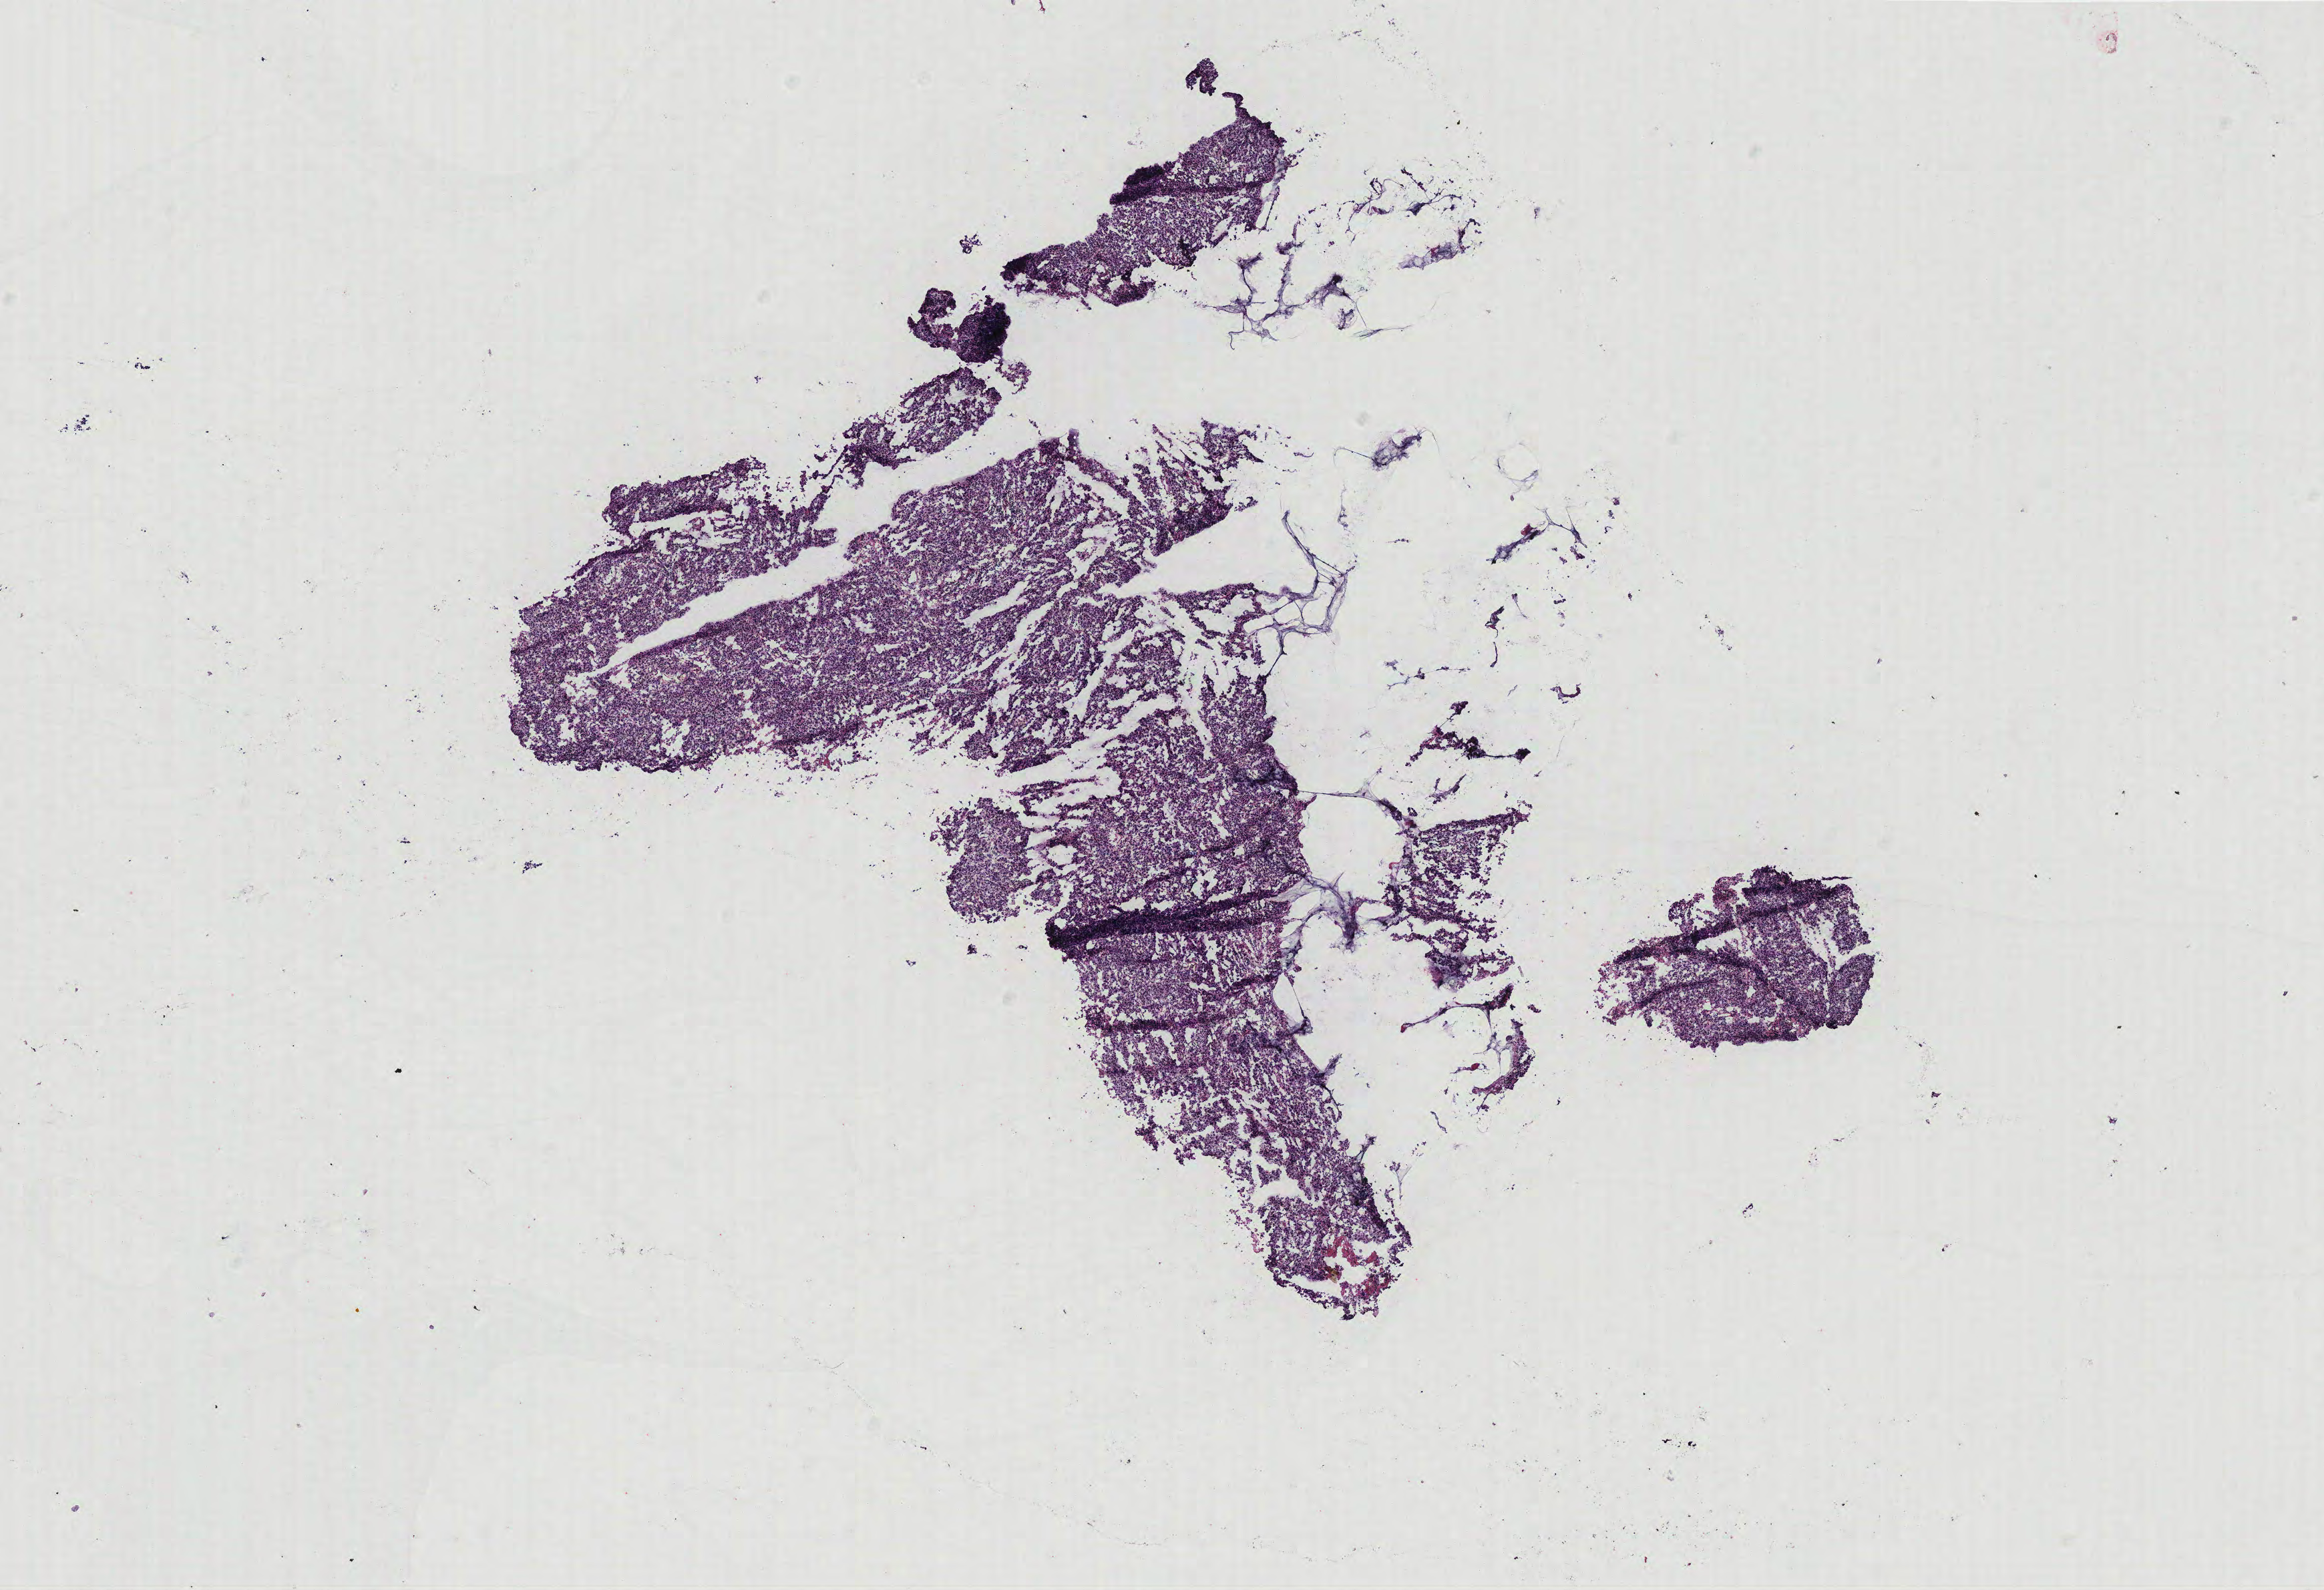
Digitized H&E-stained tissue section (whole slide) — low-resolution overview of the scanned area, about 13.9 x 9.5 mm (acquisition: 40x scan), tumour tissue sample, breast. Patient: female, age 61 years.
AJCC pathologic stage: IIA. Diagnosis: Infiltrating duct carcinoma, NOS.